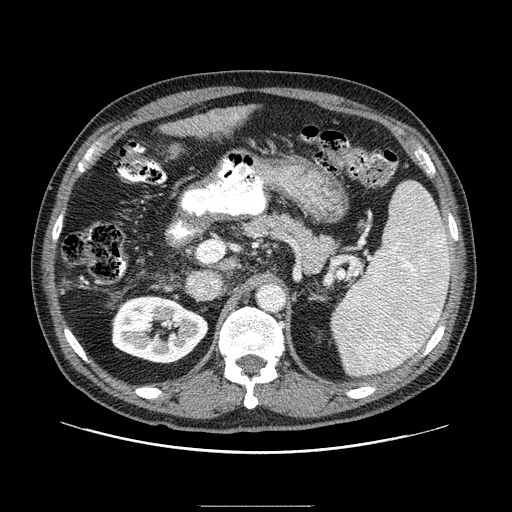
Contrast-enhanced abdominal CT (liver protocol), one axial slice; slice 42 of 99 in the series (ordered by position); one of 2 acquisitions stored at this slice position; soft-tissue window (W 400 / L 40 HU); 512 × 512 image matrix, field of view 400 × 400 mm. Case-level facts recorded for this patient, not image findings: diagnosis: hepatocellular carcinoma (patient treated with transarterial chemoembolisation; whether this scan precedes or follows treatment is not stated here); TNM stage (as recorded): Stage-II; Child-Pugh class: A; tumour differentiation: well differentiated; tumour nodularity: multinodular.
Outlined on this slice (semi-automatic segmentation, software-assisted and operator-edited):
- liver parenchyma outside the tumour (the mass and vessels are separate outlines, so this box may not span the whole liver): box from (x=175, y=106) to (x=250, y=137) px